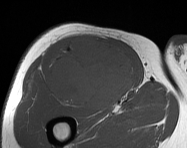
MRI of an extremity soft-tissue mass, one axial slice. Position 94 of 114 along the scan axis. MR volume resampled by the dataset authors to the PET/CT grid (not the native acquisition matrix). 3.27 mm slice thickness. 187 × 148 image matrix. Male patient. From the clinical record (not read from this slice): histological type: pleiomorphic leiomyosarcoma; grade: intermediate; site of the primary tumour: right thigh.
Annotated regions visible in this slice (expert contour drawn on MRI and transferred to this co-registered scan by the dataset authors):
- gross tumour volume including surrounding oedema: bounding box [x1, y1, x2, y2] px = [47, 36, 137, 110]
- gross tumour volume (mass): [47, 36, 137, 110]